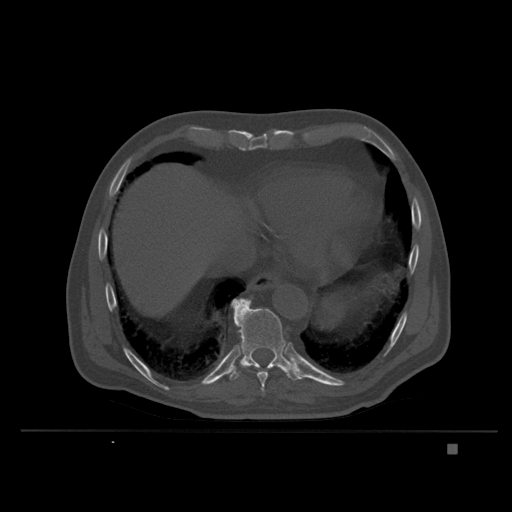
CT including the spine, one axial slice. Position 201 of 435 along the scan axis. Bone window (W 1800 / L 400 HU). 1.5 mm slice thickness. 512 × 512 image matrix. Patient: male, 73 years. From the clinical record (not read from this slice): primary cancer: skin.
Structures marked on this image (semi-automatically segmented with operator editing):
- T10 vertebra: bounding box <229,299,303,381> (left, top, right, bottom; pixels)
- T9 vertebra: <232,299,270,396>